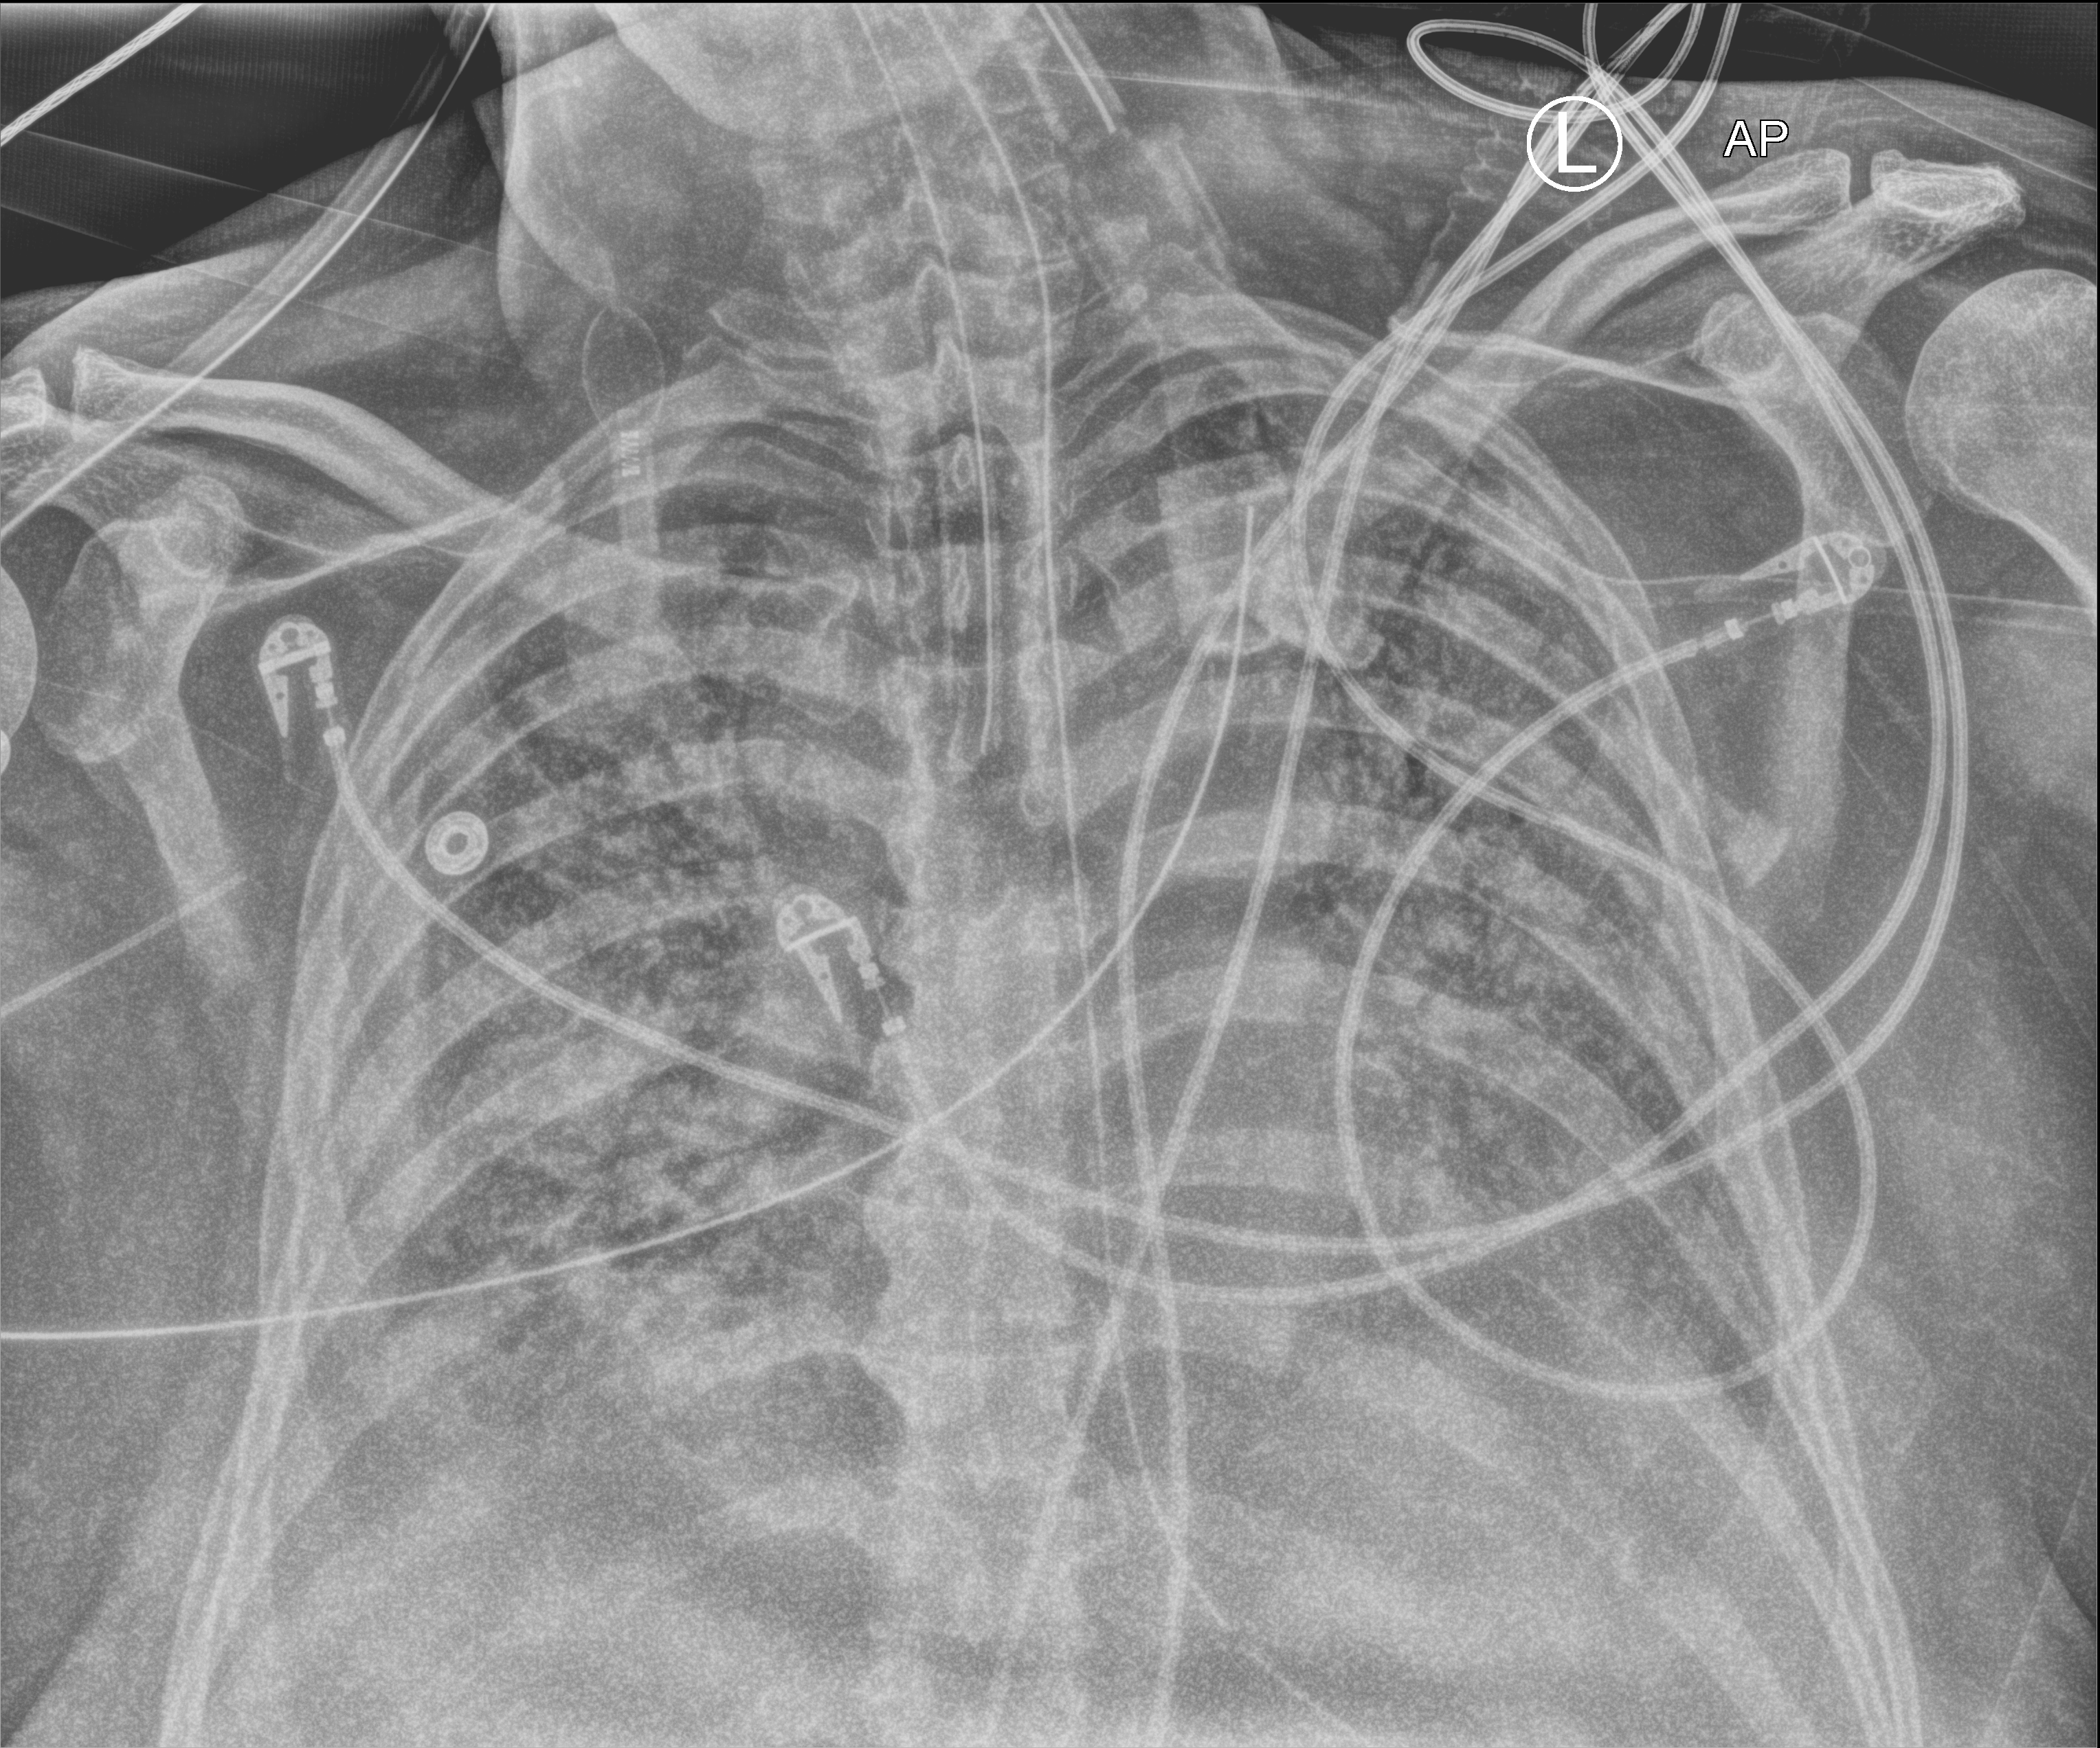
Bedside chest radiograph (computed radiography); anteroposterior (AP) projection. Patient hospitalised with COVID-19; male, aged 60–74 years.
From the hospital-stay record, not from the radiograph (when in the stay this image was taken is not recorded): COPD (admission record): no; mechanically ventilated during this hospital stay: yes; admitted to intensive care during this hospital stay: yes.